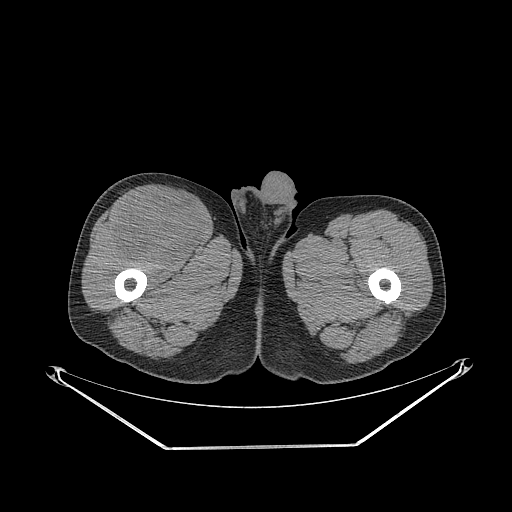
CT of an extremity soft-tissue mass (from a PET/CT study), one axial slice; 140 kVp; soft-tissue window (W 400 / L 40 HU); 512 × 512 image matrix, field of view 500 × 500 mm. Male patient. From the clinical record (not read from this slice): histological type: pleiomorphic leiomyosarcoma; grade: intermediate; site of the primary tumour: right thigh.
Outlined on this slice (expert contour drawn on MRI and transferred to this co-registered scan by the dataset authors):
- gross tumour volume including surrounding oedema: bounding box <114,191,204,264> (left, top, right, bottom; pixels)
- gross tumour volume (mass): <116,192,204,264>